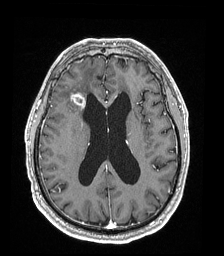
Brain MRI from a brain-tumour surgery series, one axial slice. Slice 81 of 192 in the series (ordered by position). T1-weighted post-contrast. 1 mm slice thickness. 224 × 256 image matrix. From the clinical record (not read from this slice): histopathology: Astrocytoma; WHO grade: 4; IDH mutation: yes.
Annotated regions visible in this slice (outlined manually by an expert reader):
- tumour: bounding box [x1, y1, x2, y2] px = [70, 93, 86, 110]